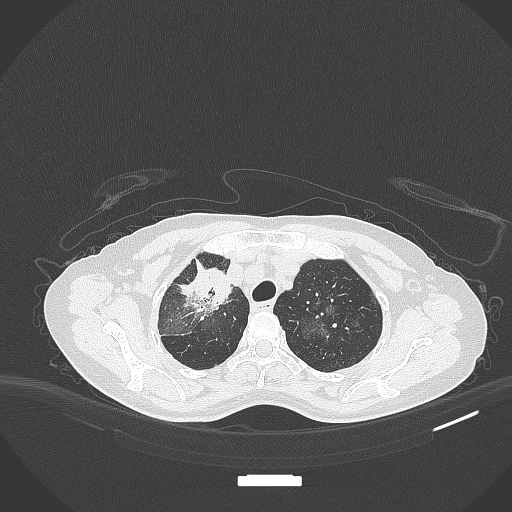
Chest CT, one axial slice; slice 265 of 284 in the series (ordered by position); 120 kVp; lung window (W 1500 / L -600 HU); 512 × 512 image matrix, field of view 400 × 400 mm. Patient: female, 59 years. Case-level facts recorded for this patient, not image findings: clinical TNM (as recorded): T3 N0 M0.
Outlined on this slice (bounding box drawn by a radiologist):
- lung tumour (recorded histology: adenocarcinoma): bounding box (x1, y1, x2, y2) in pixels: (174, 263, 234, 318)